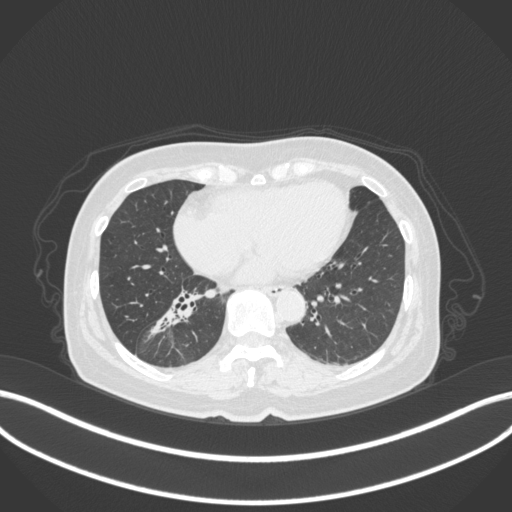
Chest CT, one axial slice; slice 150 of 429 in the series (ordered by position); lung window (W 1500 / L -600 HU); 1 mm slice thickness; 512 × 512 image matrix, field of view 400 × 400 mm. Patient: female, 67 years. From the clinical record (not read from this slice): clinical TNM (as recorded): T1c N1 M0; histopathological grade: G2-3.
Annotated regions visible in this slice (bounding box drawn by a radiologist):
- lung tumour (recorded histology: adenocarcinoma): bounding box (x1, y1, x2, y2) in pixels: (147, 293, 197, 334)